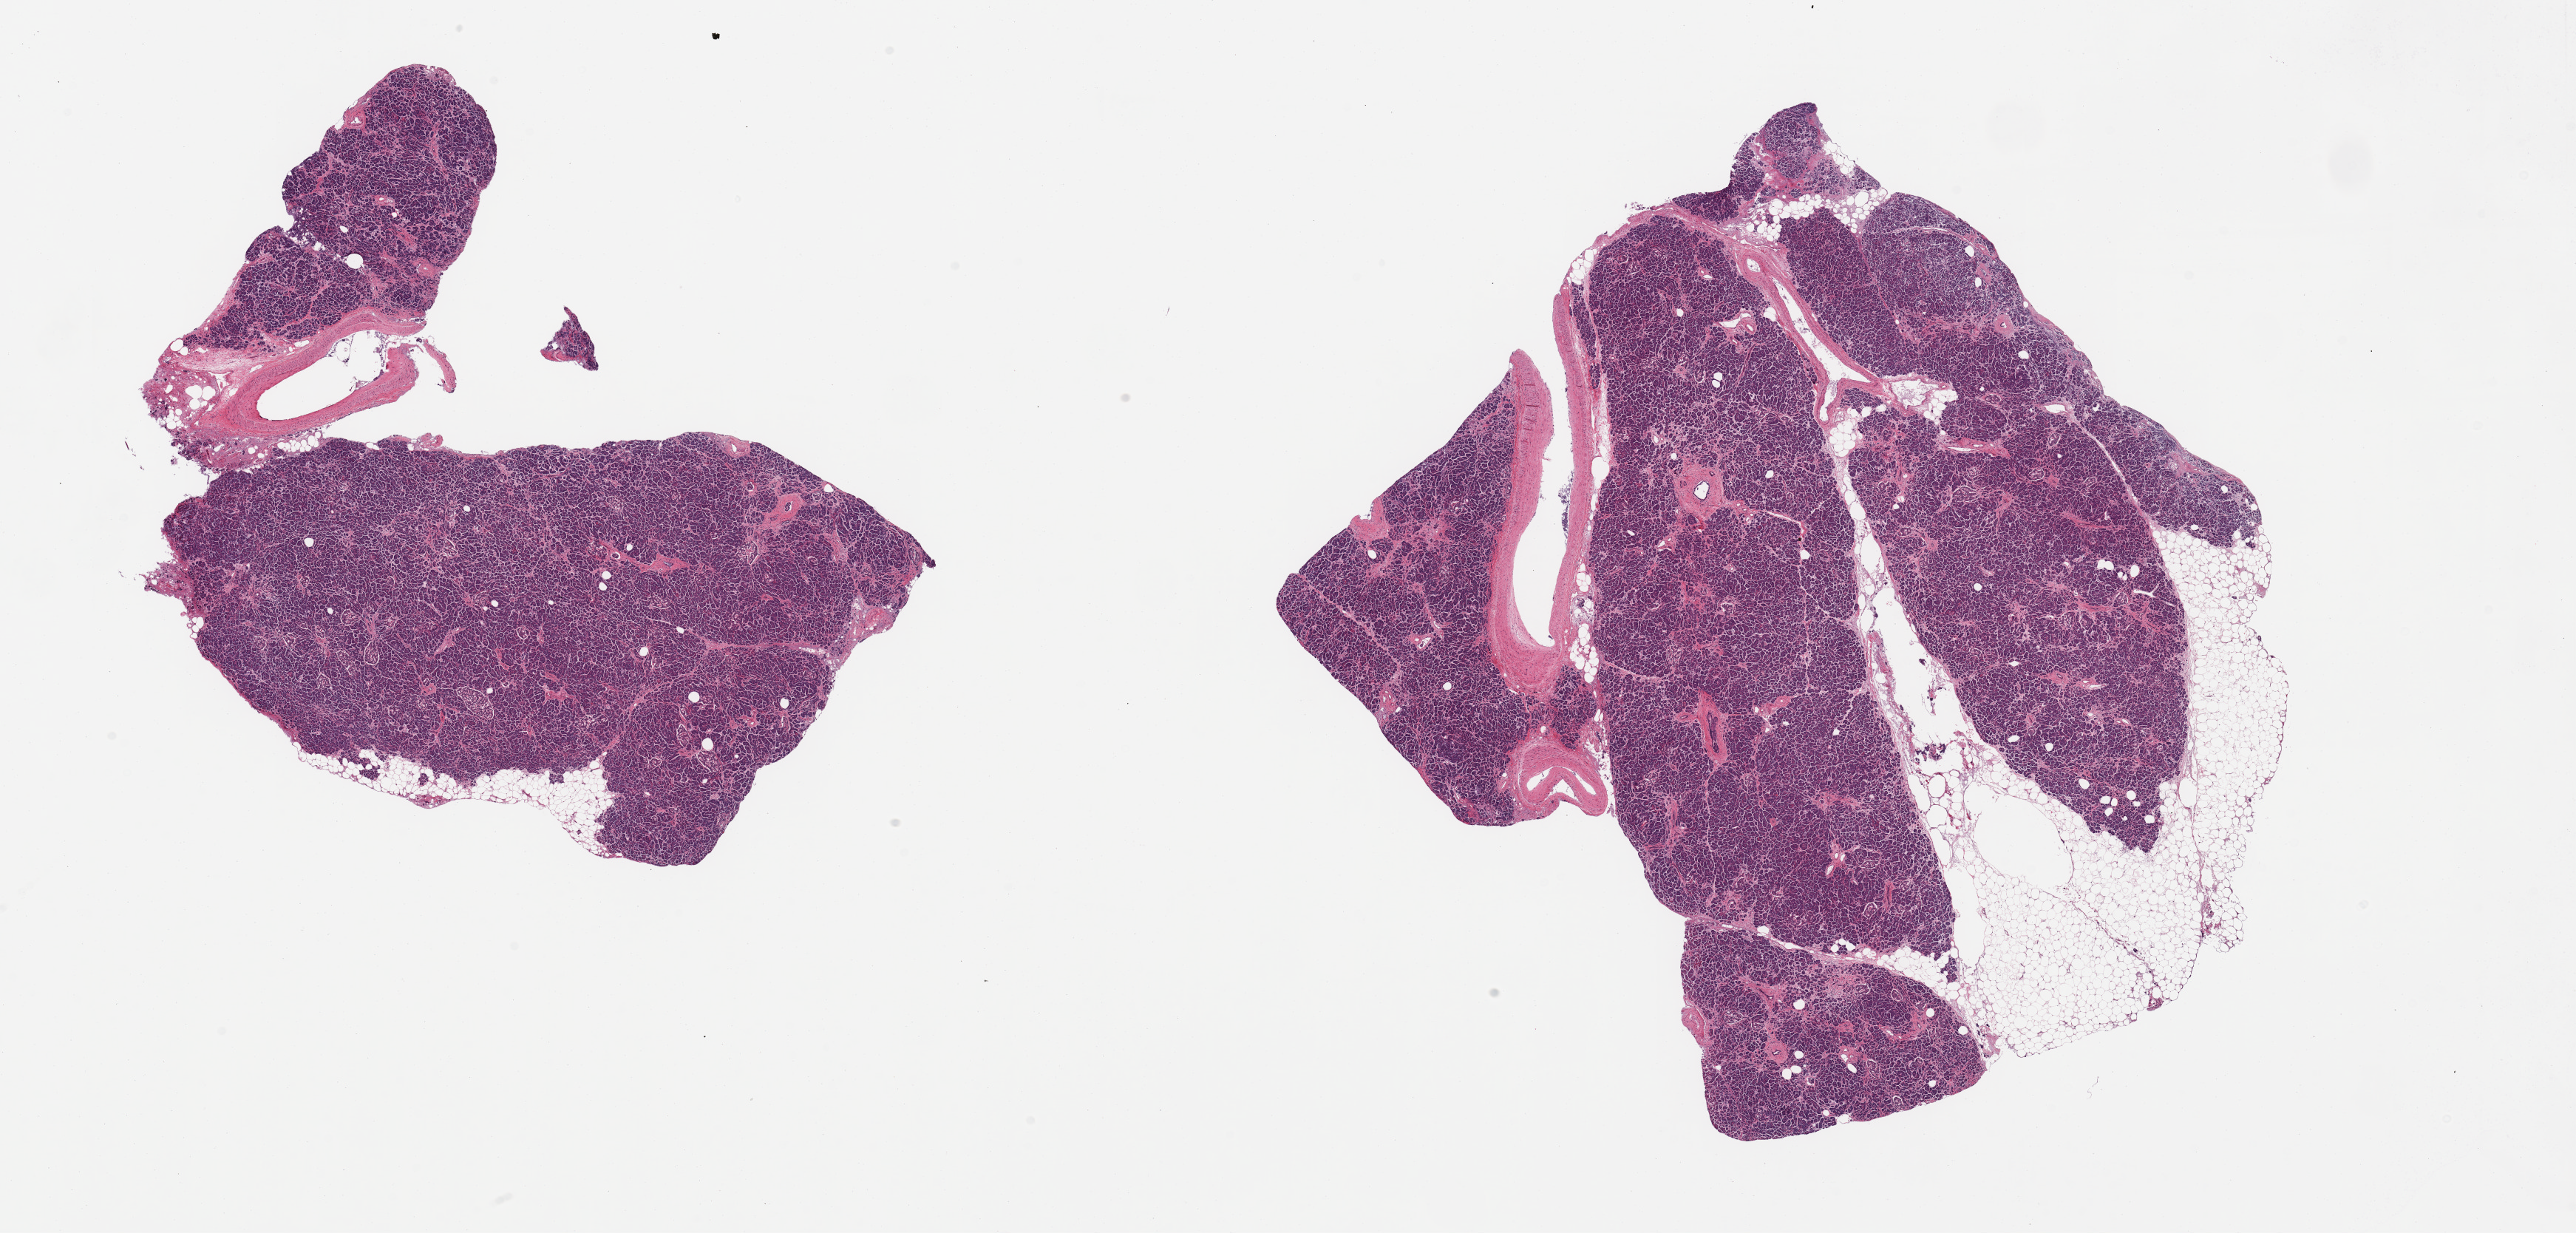
H&E whole-slide image, whole scanned area (about 27.6 x 13.2 mm, acquisition: 20x scan) shown as a low-resolution overview, PAXgene-fixed, paraffin-embedded tissue, sampled site (target tissue): pancreas, tissue donor sample. Male donor.
Reviewer comment on this tissue sample: 2 pieces; well preserved with islets; less than 10% and ~15% of external fat.